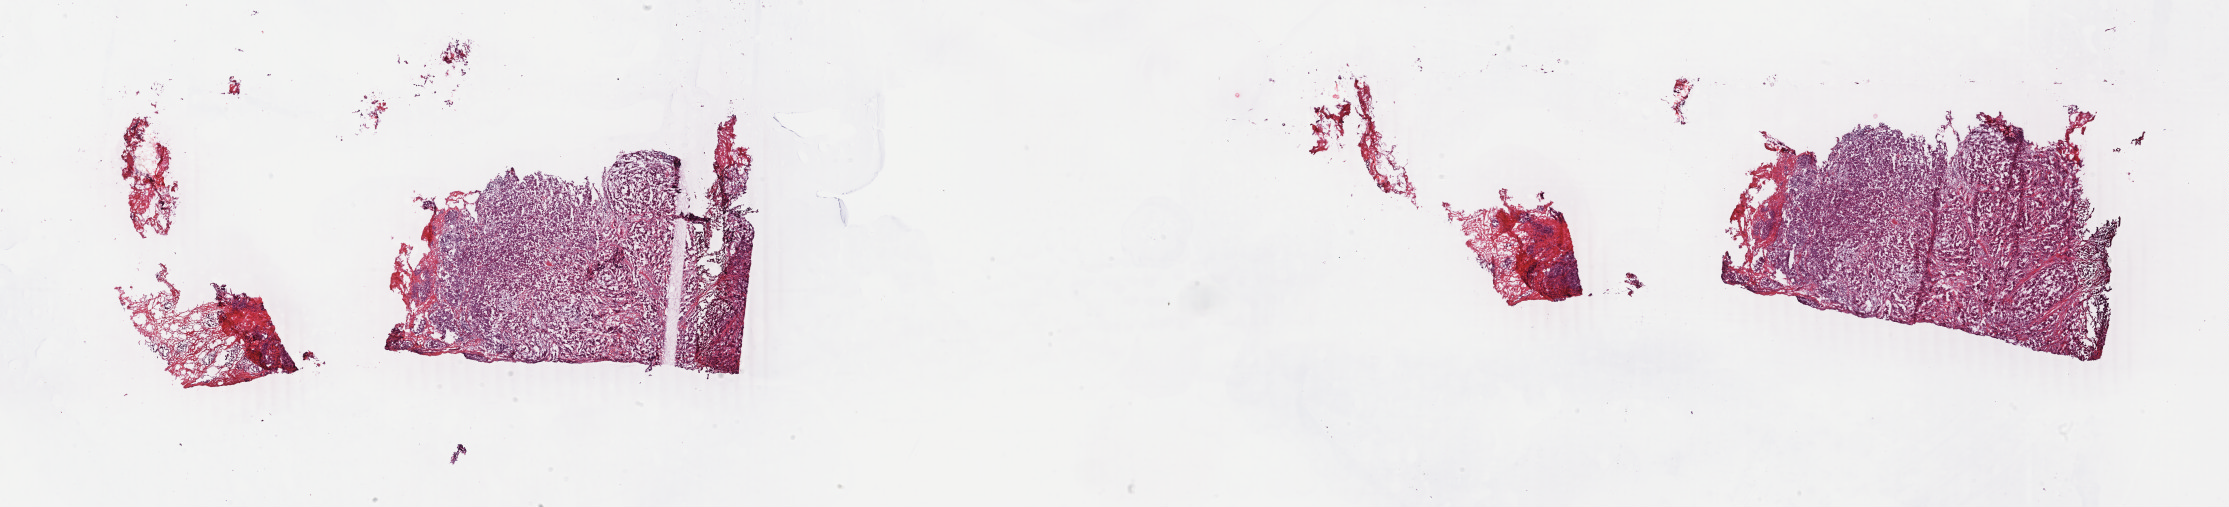
Digitized Hematoxylin and eosin (H&E) stained tissue section (whole slide), low-resolution overview of the scanned area, about 35.5 x 8.1 mm; frozen section from the bottom of the tissue portion; breast, primary tumour sample. Patient: female, age at initial diagnosis 53 years. Slide review estimates, as recorded: tumour cells 80%, tumour nuclei 80%, normal cells 2%, stromal cells 17%, necrosis 1%. Inflammatory infiltration, as recorded: lymphocyte infiltration 2%, monocyte infiltration 0%, neutrophil infiltration 0%.
Lymph nodes positive (case pathology): 1 of 13 examined. Diagnosis: Infiltrating duct carcinoma, NOS. Laterality: right. AJCC pathologic stage: IIB.